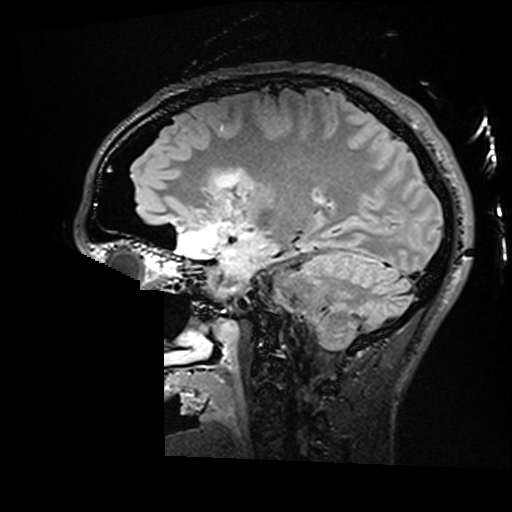
Brain MRI from a brain-tumour surgery series, one sagittal slice; position 103 of 176 along the scan axis; T2 FLAIR; 1 mm slice thickness; 512 × 512 image matrix, field of view 250 × 250 mm. Case-level facts recorded for this patient, not image findings: histopathology: Astrocytoma; WHO grade: 2; IDH mutation: yes; tumour location: Right Insular.
Structures marked on this image (expert manual segmentation):
- residual tumour: bounding box <216,170,245,189> (left, top, right, bottom; pixels)